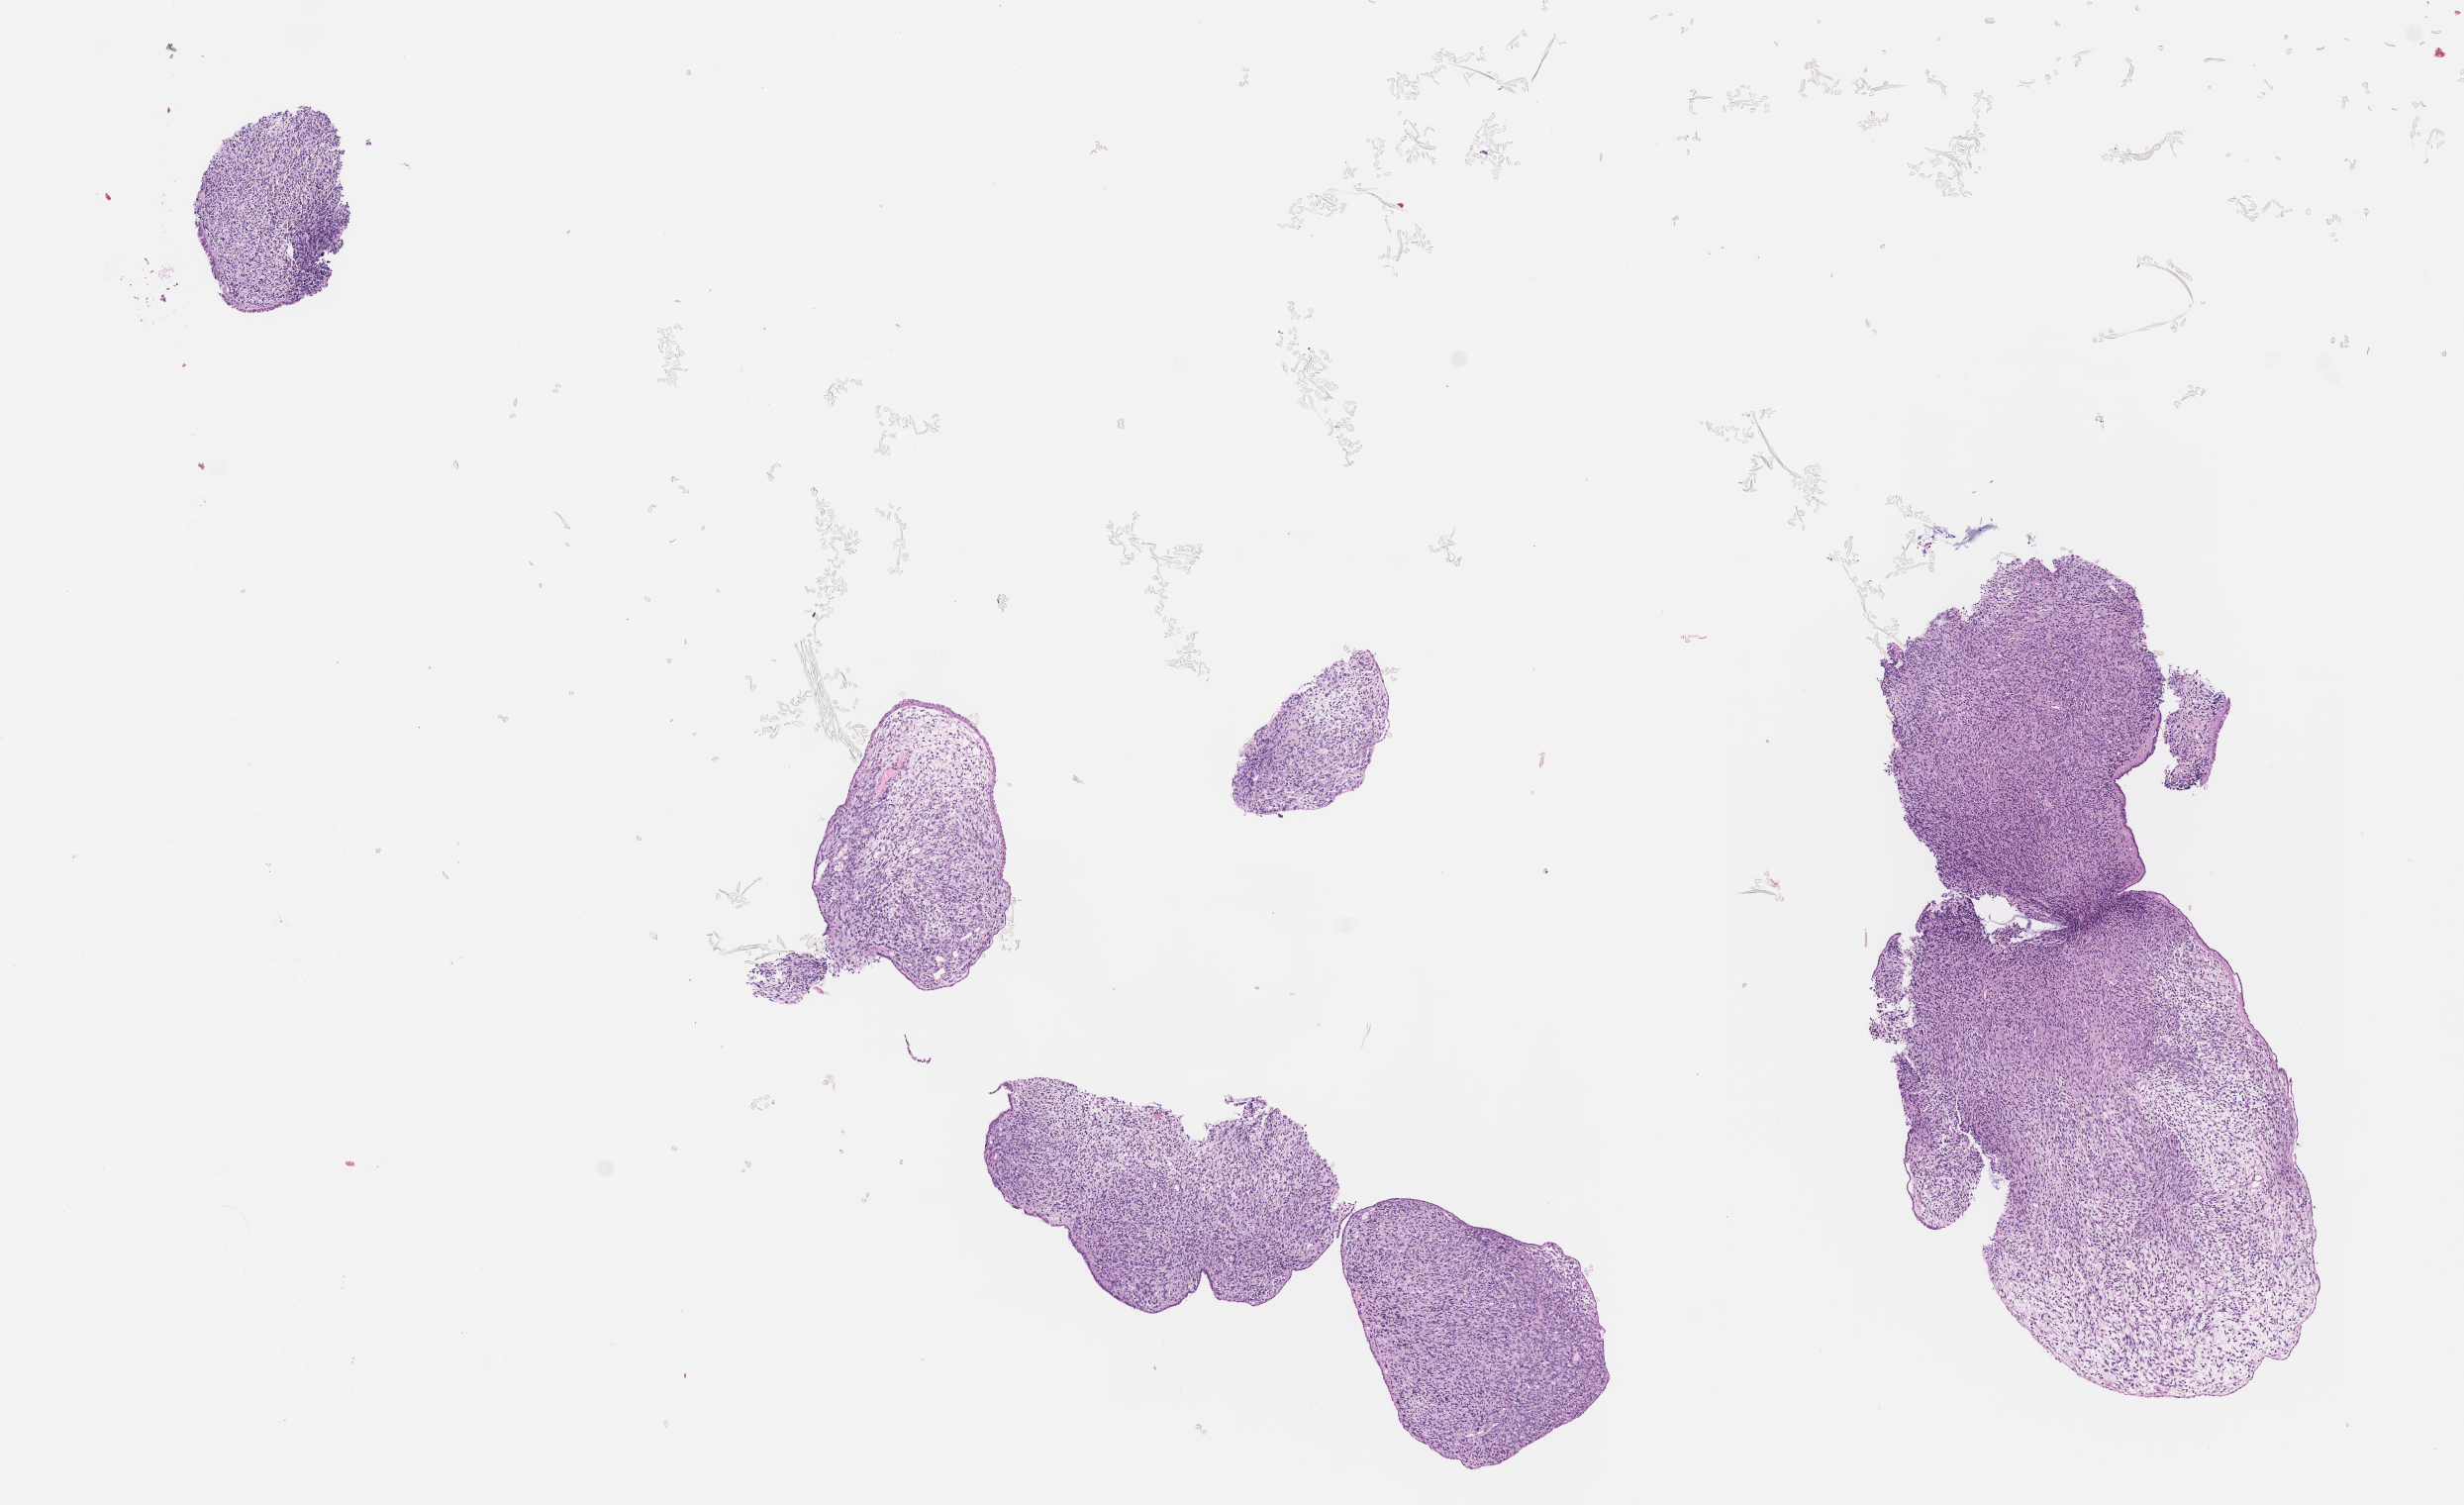
H&E whole-slide image of tumor tissue — a low-resolution overview of the entire scanned area, about 10.1 x 6.1 mm; FFPE section; site: left ear. Male patient, age at diagnosis 2.5 years.
Metastatic status at presentation (as recorded): non-metastatic (confirmed). Stage (as recorded): 2. Diagnosis: rhabdomyosarcoma; histological classification: embryonal rhabdomyosarcoma.